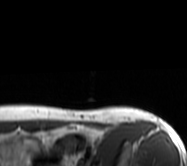
MRI of an extremity soft-tissue mass, one axial slice. MR volume resampled by the dataset authors to the PET/CT grid (not the native acquisition matrix). 3.27 mm slice thickness. 187 × 166 image matrix, field of view 183 × 162 mm. Female patient. From the clinical record (not read from this slice): histological type: leiomyosarcoma; grade: high; site of the primary tumour: groin.
Structures marked on this image (expert contour drawn on MRI and transferred to this co-registered scan by the dataset authors):
- gross tumour volume including surrounding oedema: bounding box [x1, y1, x2, y2] px = [98, 106, 142, 118]